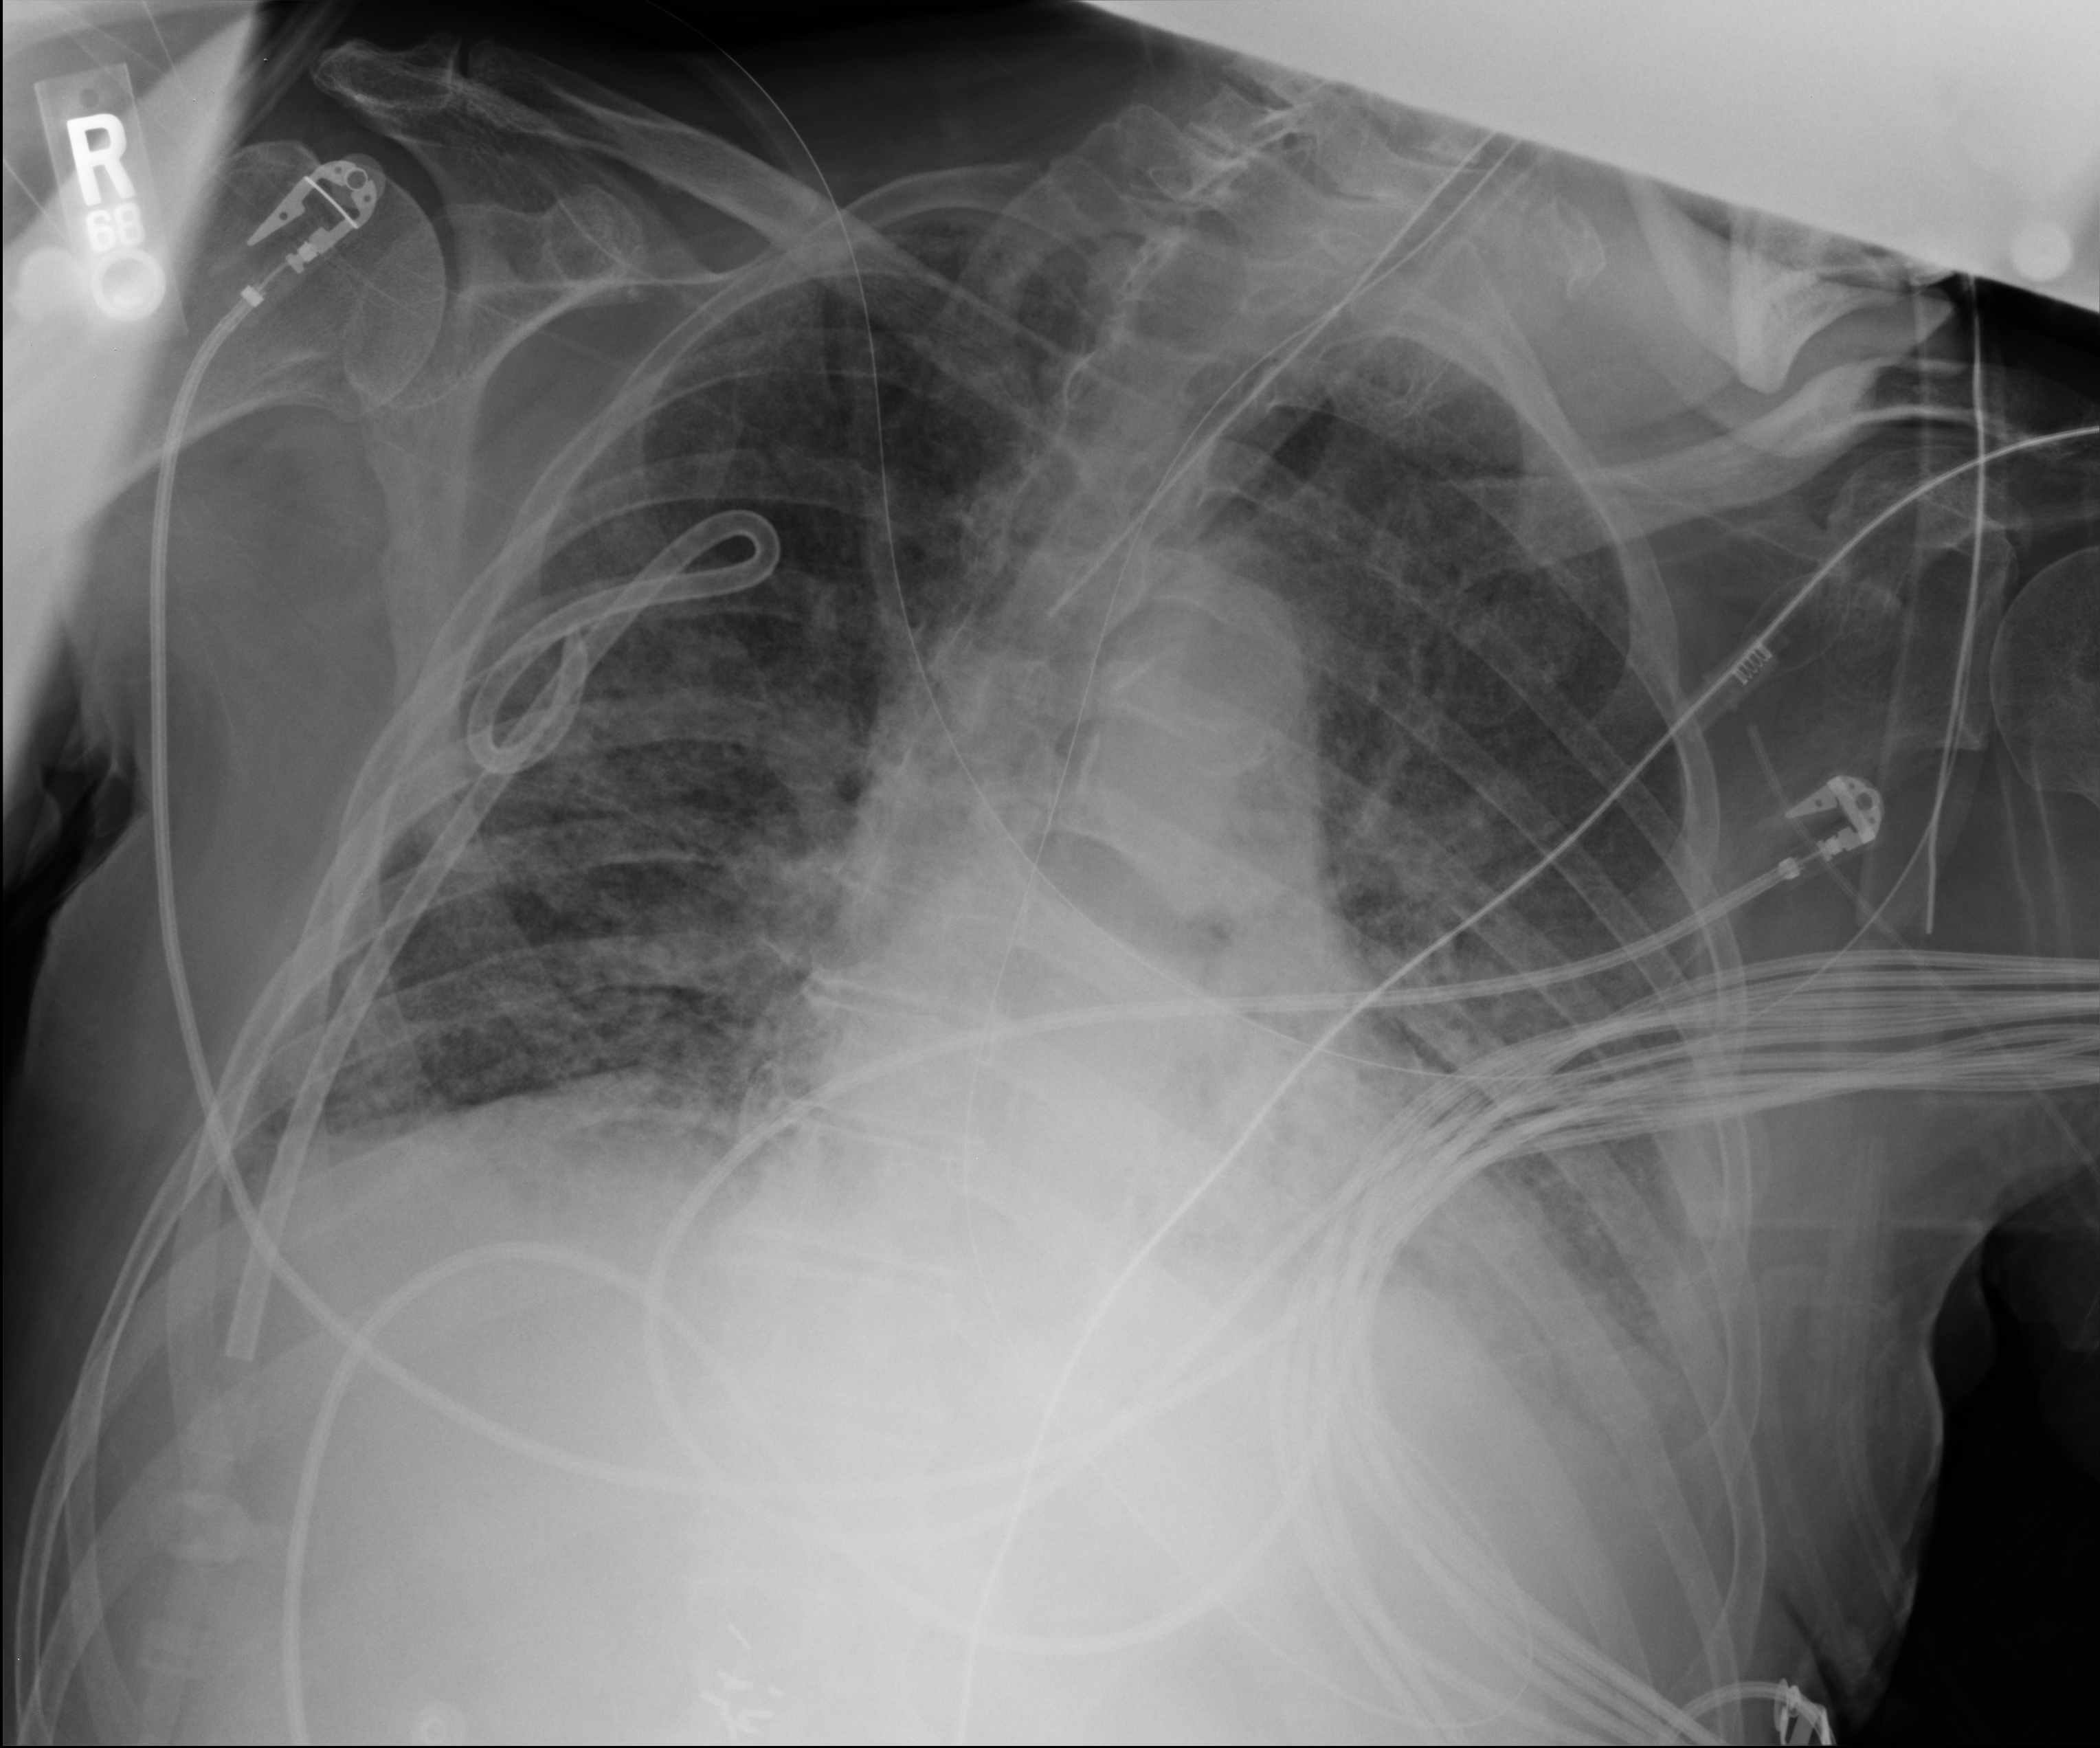
Chest X-ray (portable), anteroposterior (AP) projection. Patient hospitalised with COVID-19; male, aged 75–90 years.
From the hospital-stay record, not from the radiograph (when in the stay this image was taken is not recorded): mechanically ventilated during this hospital stay: yes.